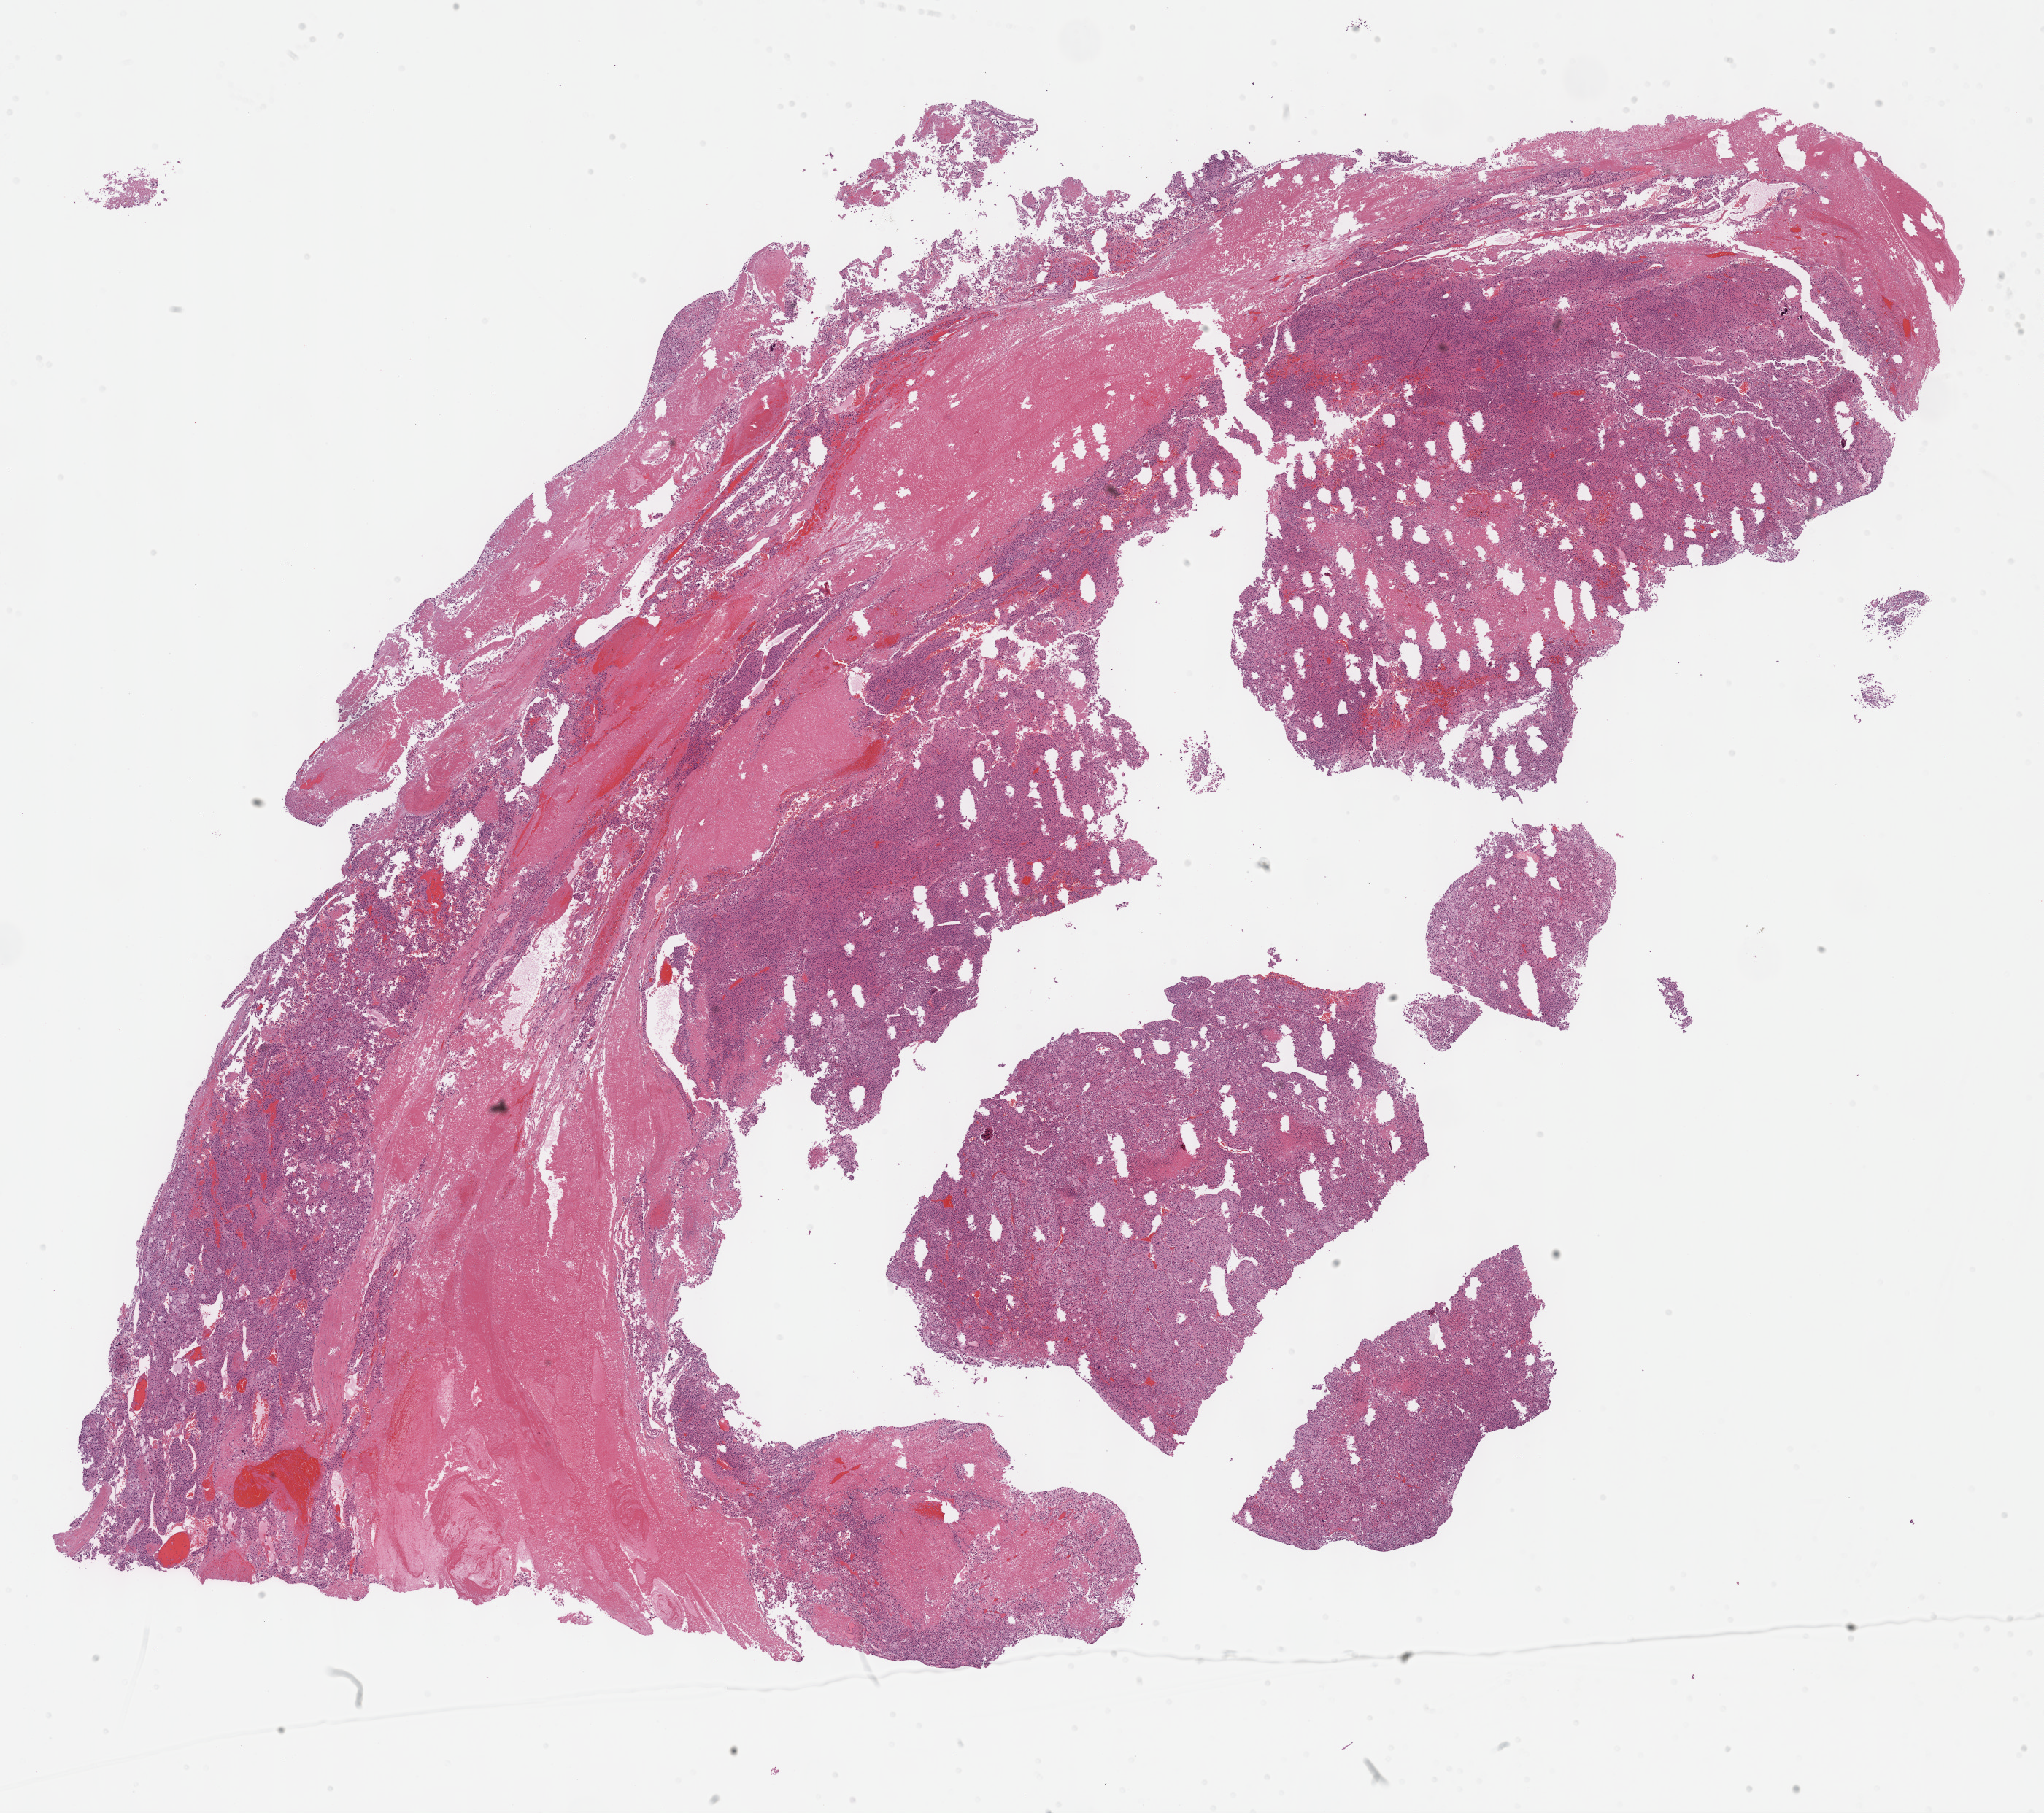
Whole-slide histology image, H&E, shown as a low-resolution overview of the whole scanned area (about 22.7 x 20.1 mm), FFPE section, sample: primary tumour, adrenal cortex. Female patient; age at initial diagnosis 68 years.
- diagnosis: Adrenal cortical carcinoma
- lymph nodes positive (case pathology): 1 of 2 examined